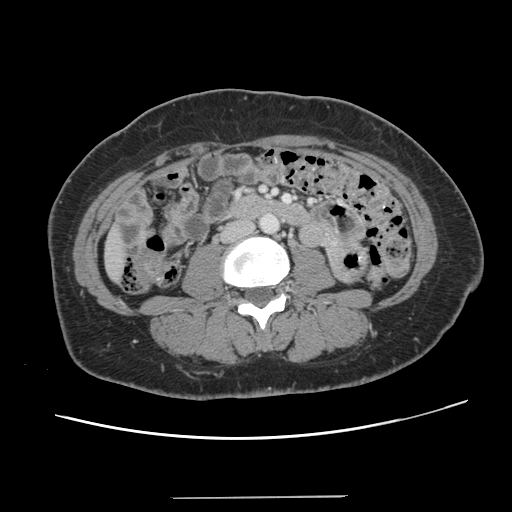
Contrast-enhanced abdominal CT, one axial slice. Slice 19 of 141 in the series (ordered by position). 120 kVp. Intravenous contrast given. Soft-tissue window (W 400 / L 40 HU). 2.5 mm slice thickness. 512 × 512 image matrix, field of view 366 × 366 mm. Female patient, age 53 years. From the clinical record (not read from this slice): diagnosis: colorectal cancer liver metastases, imaged before liver resection; multiple liver metastases: no; largest metastasis: 14.5 cm; chemotherapy before resection: yes.
Structures marked on this image (outlined manually by an expert reader):
- liver: box from (x=106, y=230) to (x=126, y=280) px
- planned liver remnant (the part of the liver to remain after resection): (x=106, y=230)–(x=126, y=280)